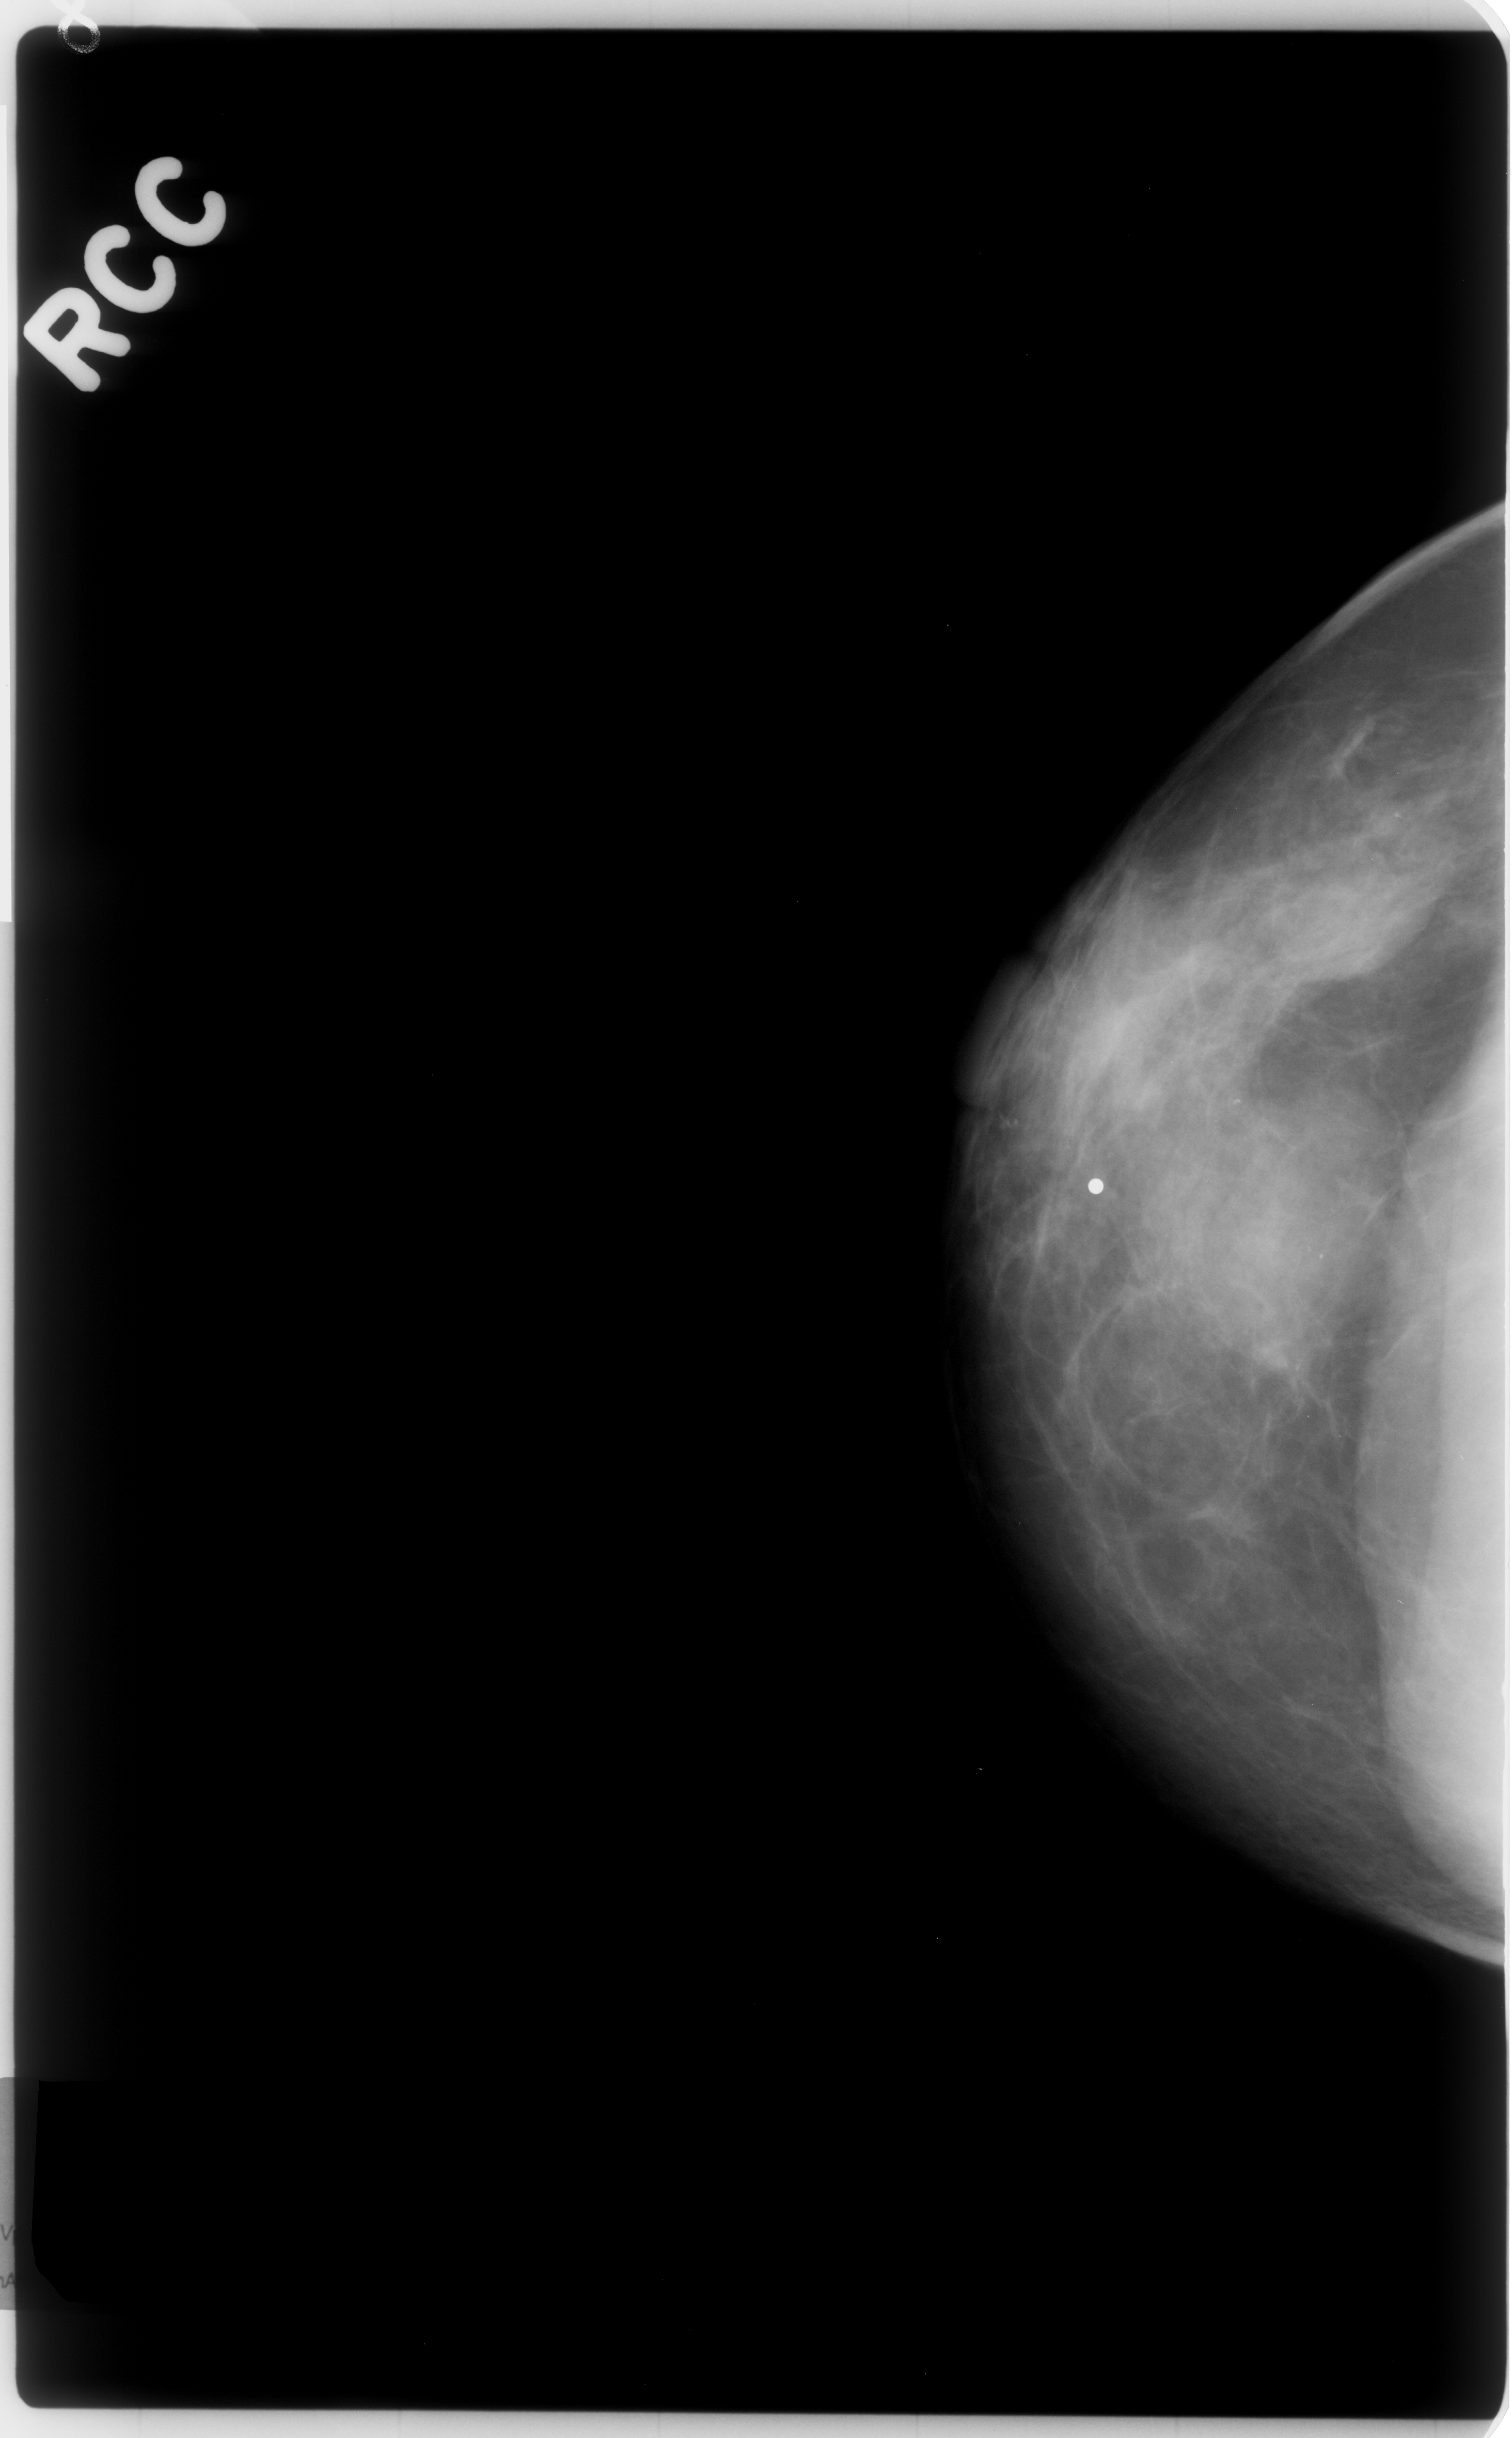
Mammogram (digitized film); right breast; CC view; breast composition: scattered fibroglandular densities (BI-RADS density category 2 of 4).
Abnormality record for this image: mass, shape oval, margins obscured; BI-RADS assessment category 3; pathology result (as recorded, not read from the image): benign.